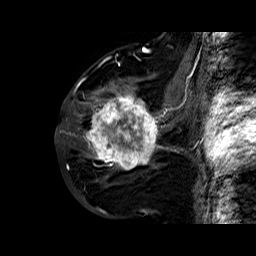
Breast MRI (dynamic contrast-enhanced), one sagittal slice. Slice 29 of 60 in the series (ordered by position). Dynamic contrast-enhanced series, time point 2 of 6 at this slice position (early post-contrast). 1.5 T. TE 6.4 ms, TR 32.8 ms. 4 mm slice thickness. 256 × 256 image matrix, field of view 200 × 200 mm. Female patient. Case-level facts recorded for this patient, not image findings: setting: breast cancer imaged before/during neoadjuvant chemotherapy; receptor status: HR-positive, HER2-negative.
Outlined on this slice (semi-automatically segmented with operator editing):
- analysis volume of interest (the breast-tissue region the enhancement analysis was run in; not a lesion): bounding box [x1, y1, x2, y2] px = [86, 77, 163, 177]
- tumour enhancement mask (voxels above the 100 % enhancement threshold inside the analysis volume of interest): [86, 87, 163, 171]